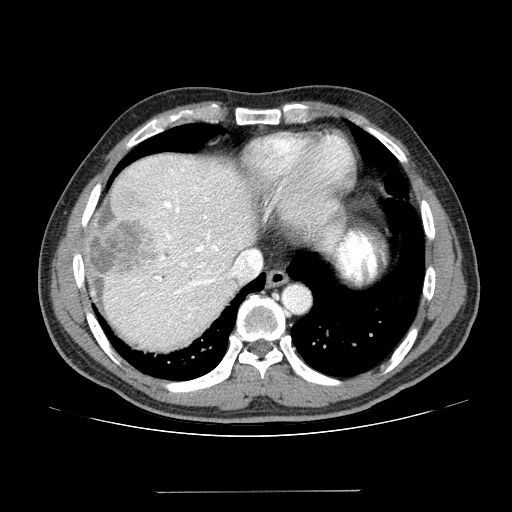
Contrast-enhanced abdominal CT (liver protocol), one axial slice; slice 113 of 131 in the series (ordered by position); reconstruction kernel STANDARD; 100 kVp; one of 2 acquisitions stored at this slice position; soft-tissue window (W 400 / L 40 HU); 2.5 mm slice thickness; 512 × 512 image matrix, field of view 380 × 380 mm. Case-level facts recorded for this patient, not image findings: diagnosis: hepatocellular carcinoma (patient treated with transarterial chemoembolisation; whether this scan precedes or follows treatment is not stated here); TNM stage (as recorded): Stage-I; Child-Pugh class: A; tumour differentiation: poorly differentiated; tumour nodularity: uninodular.
Structures marked on this image (semi-automatic segmentation, software-assisted and operator-edited):
- abdominal aorta: bounding box (x1, y1, x2, y2) in pixels: (283, 285, 310, 313)
- liver parenchyma outside the tumour (the mass and vessels are separate outlines, so this box may not span the whole liver): (84, 154, 256, 350)
- mass: (77, 216, 157, 283)
- liver vessels: (112, 161, 239, 327)